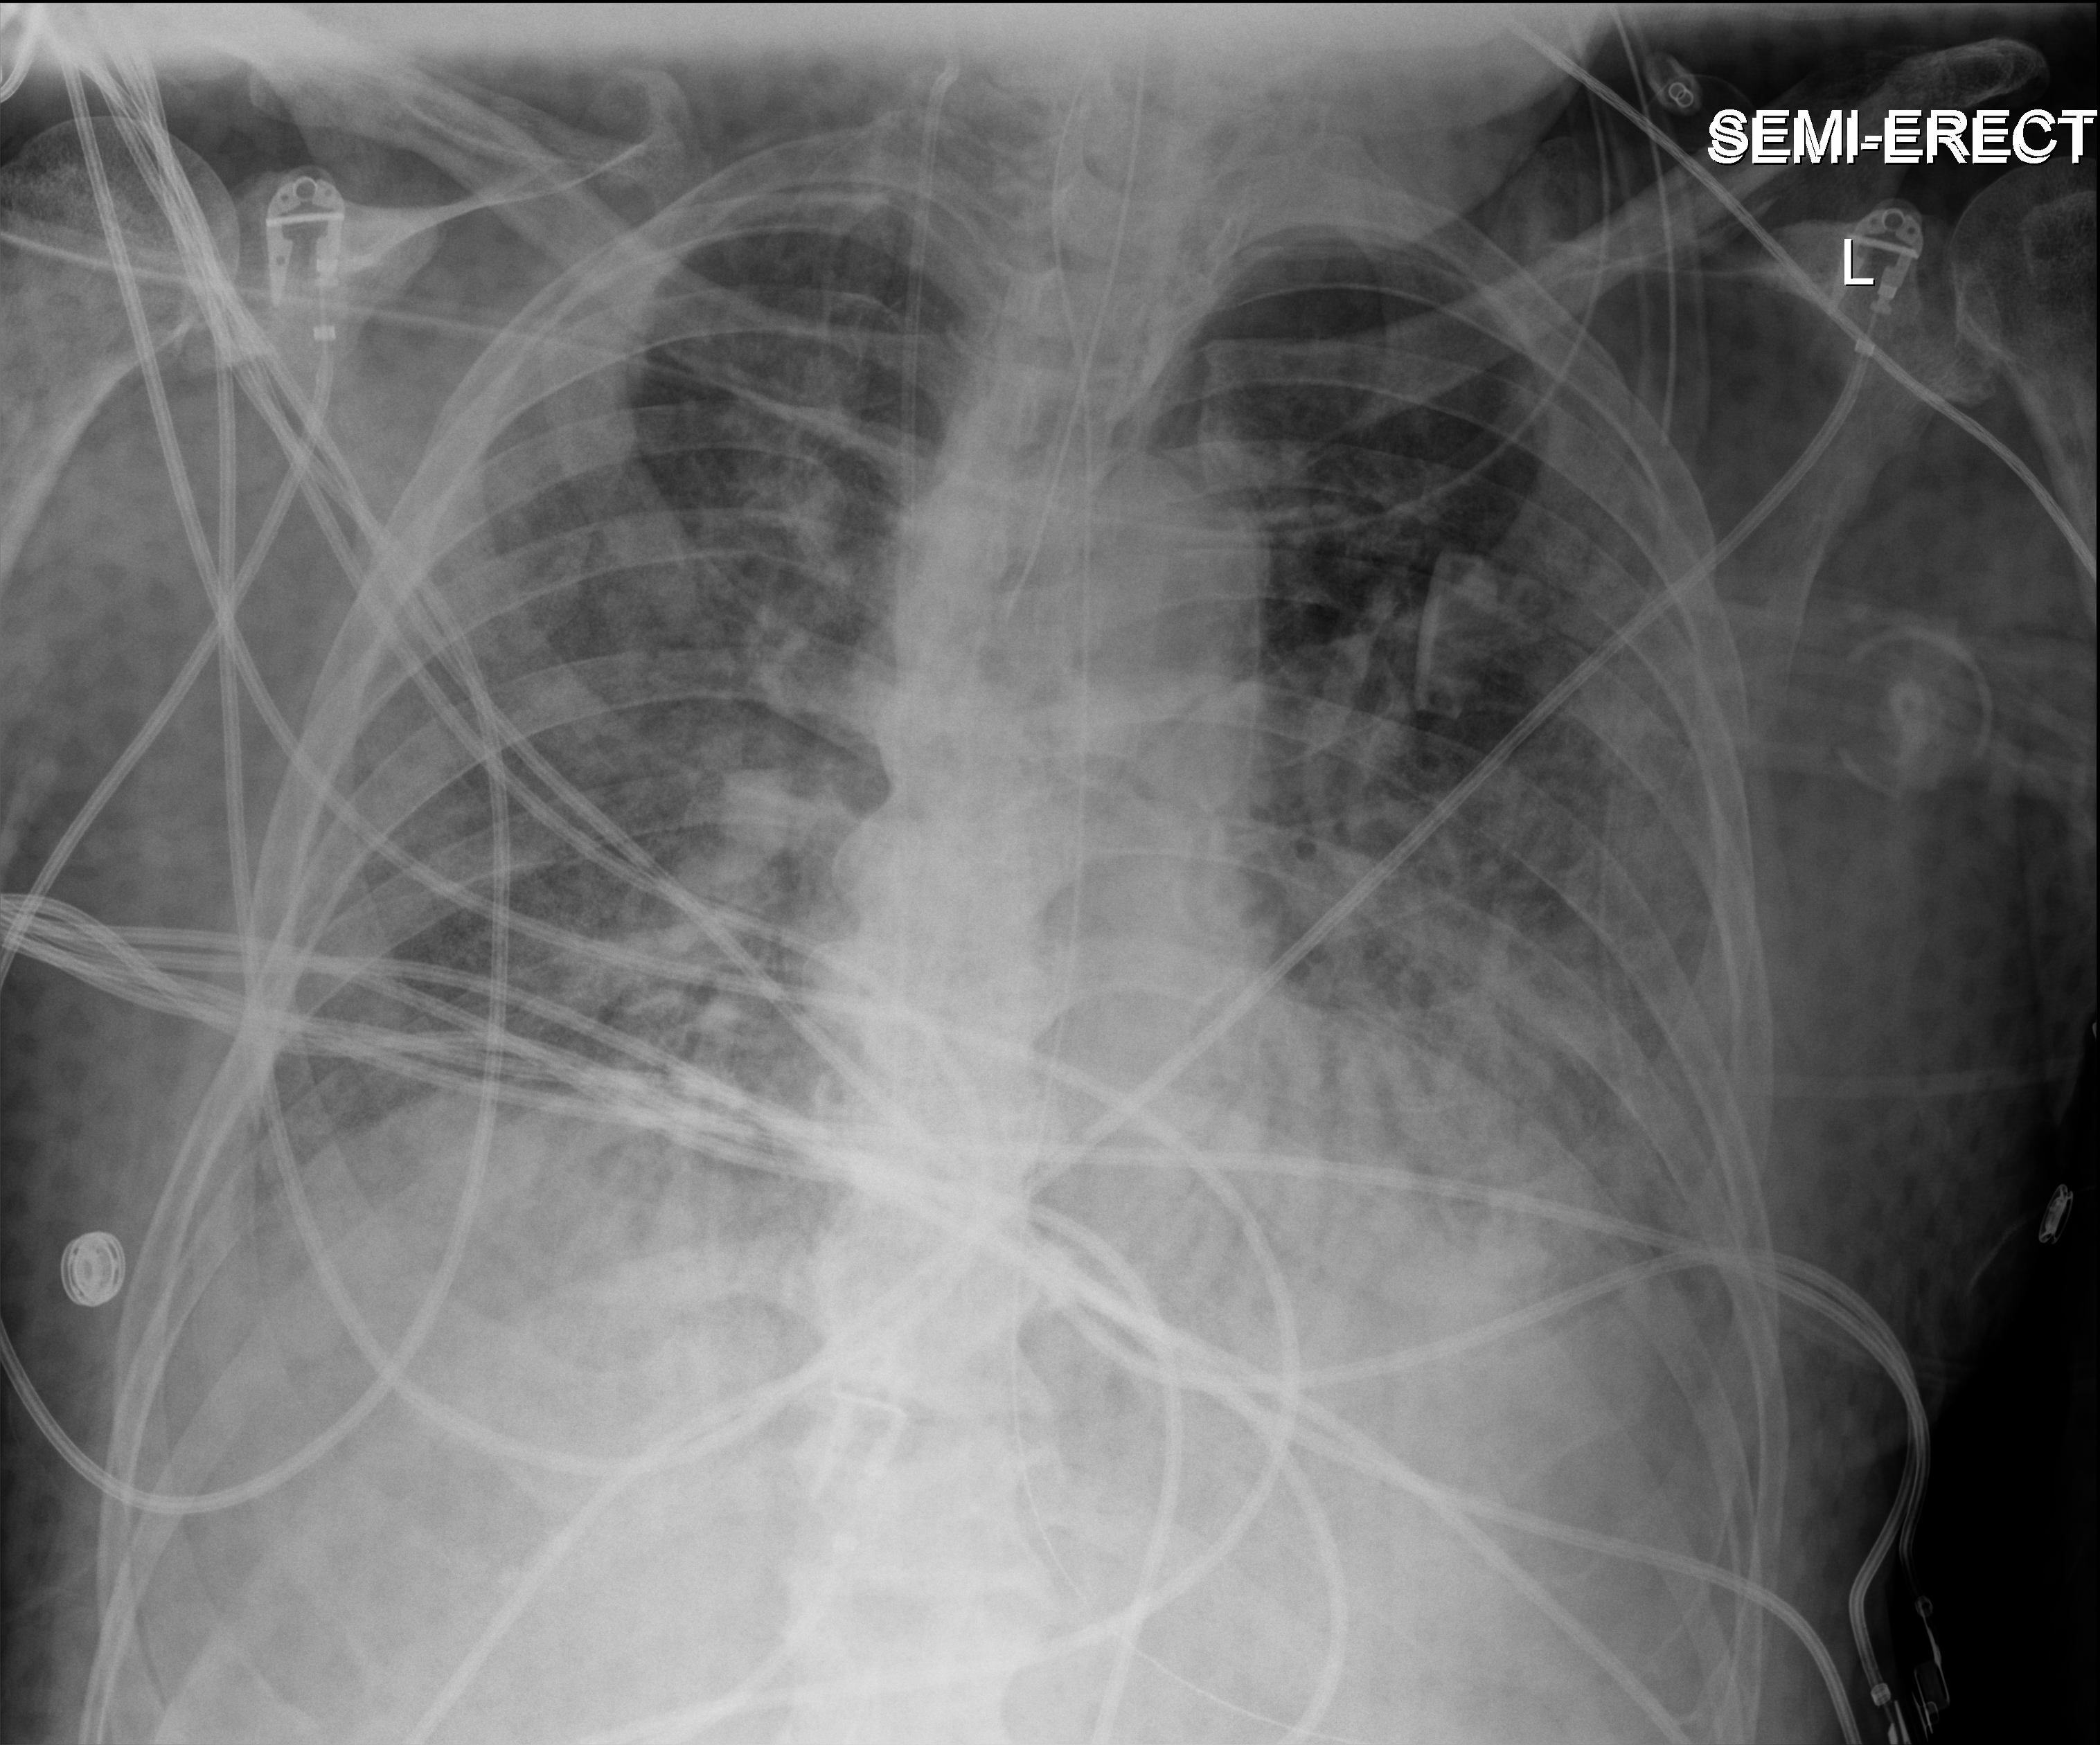
Bedside chest radiograph (digital radiography), anteroposterior (AP) projection. Male patient hospitalised with COVID-19, age 75–90 years.
Admission-level facts for this patient (not findings on this image; timing relative to this image not recorded): mechanically ventilated during this hospital stay: yes; admitted to intensive care during this hospital stay: yes.